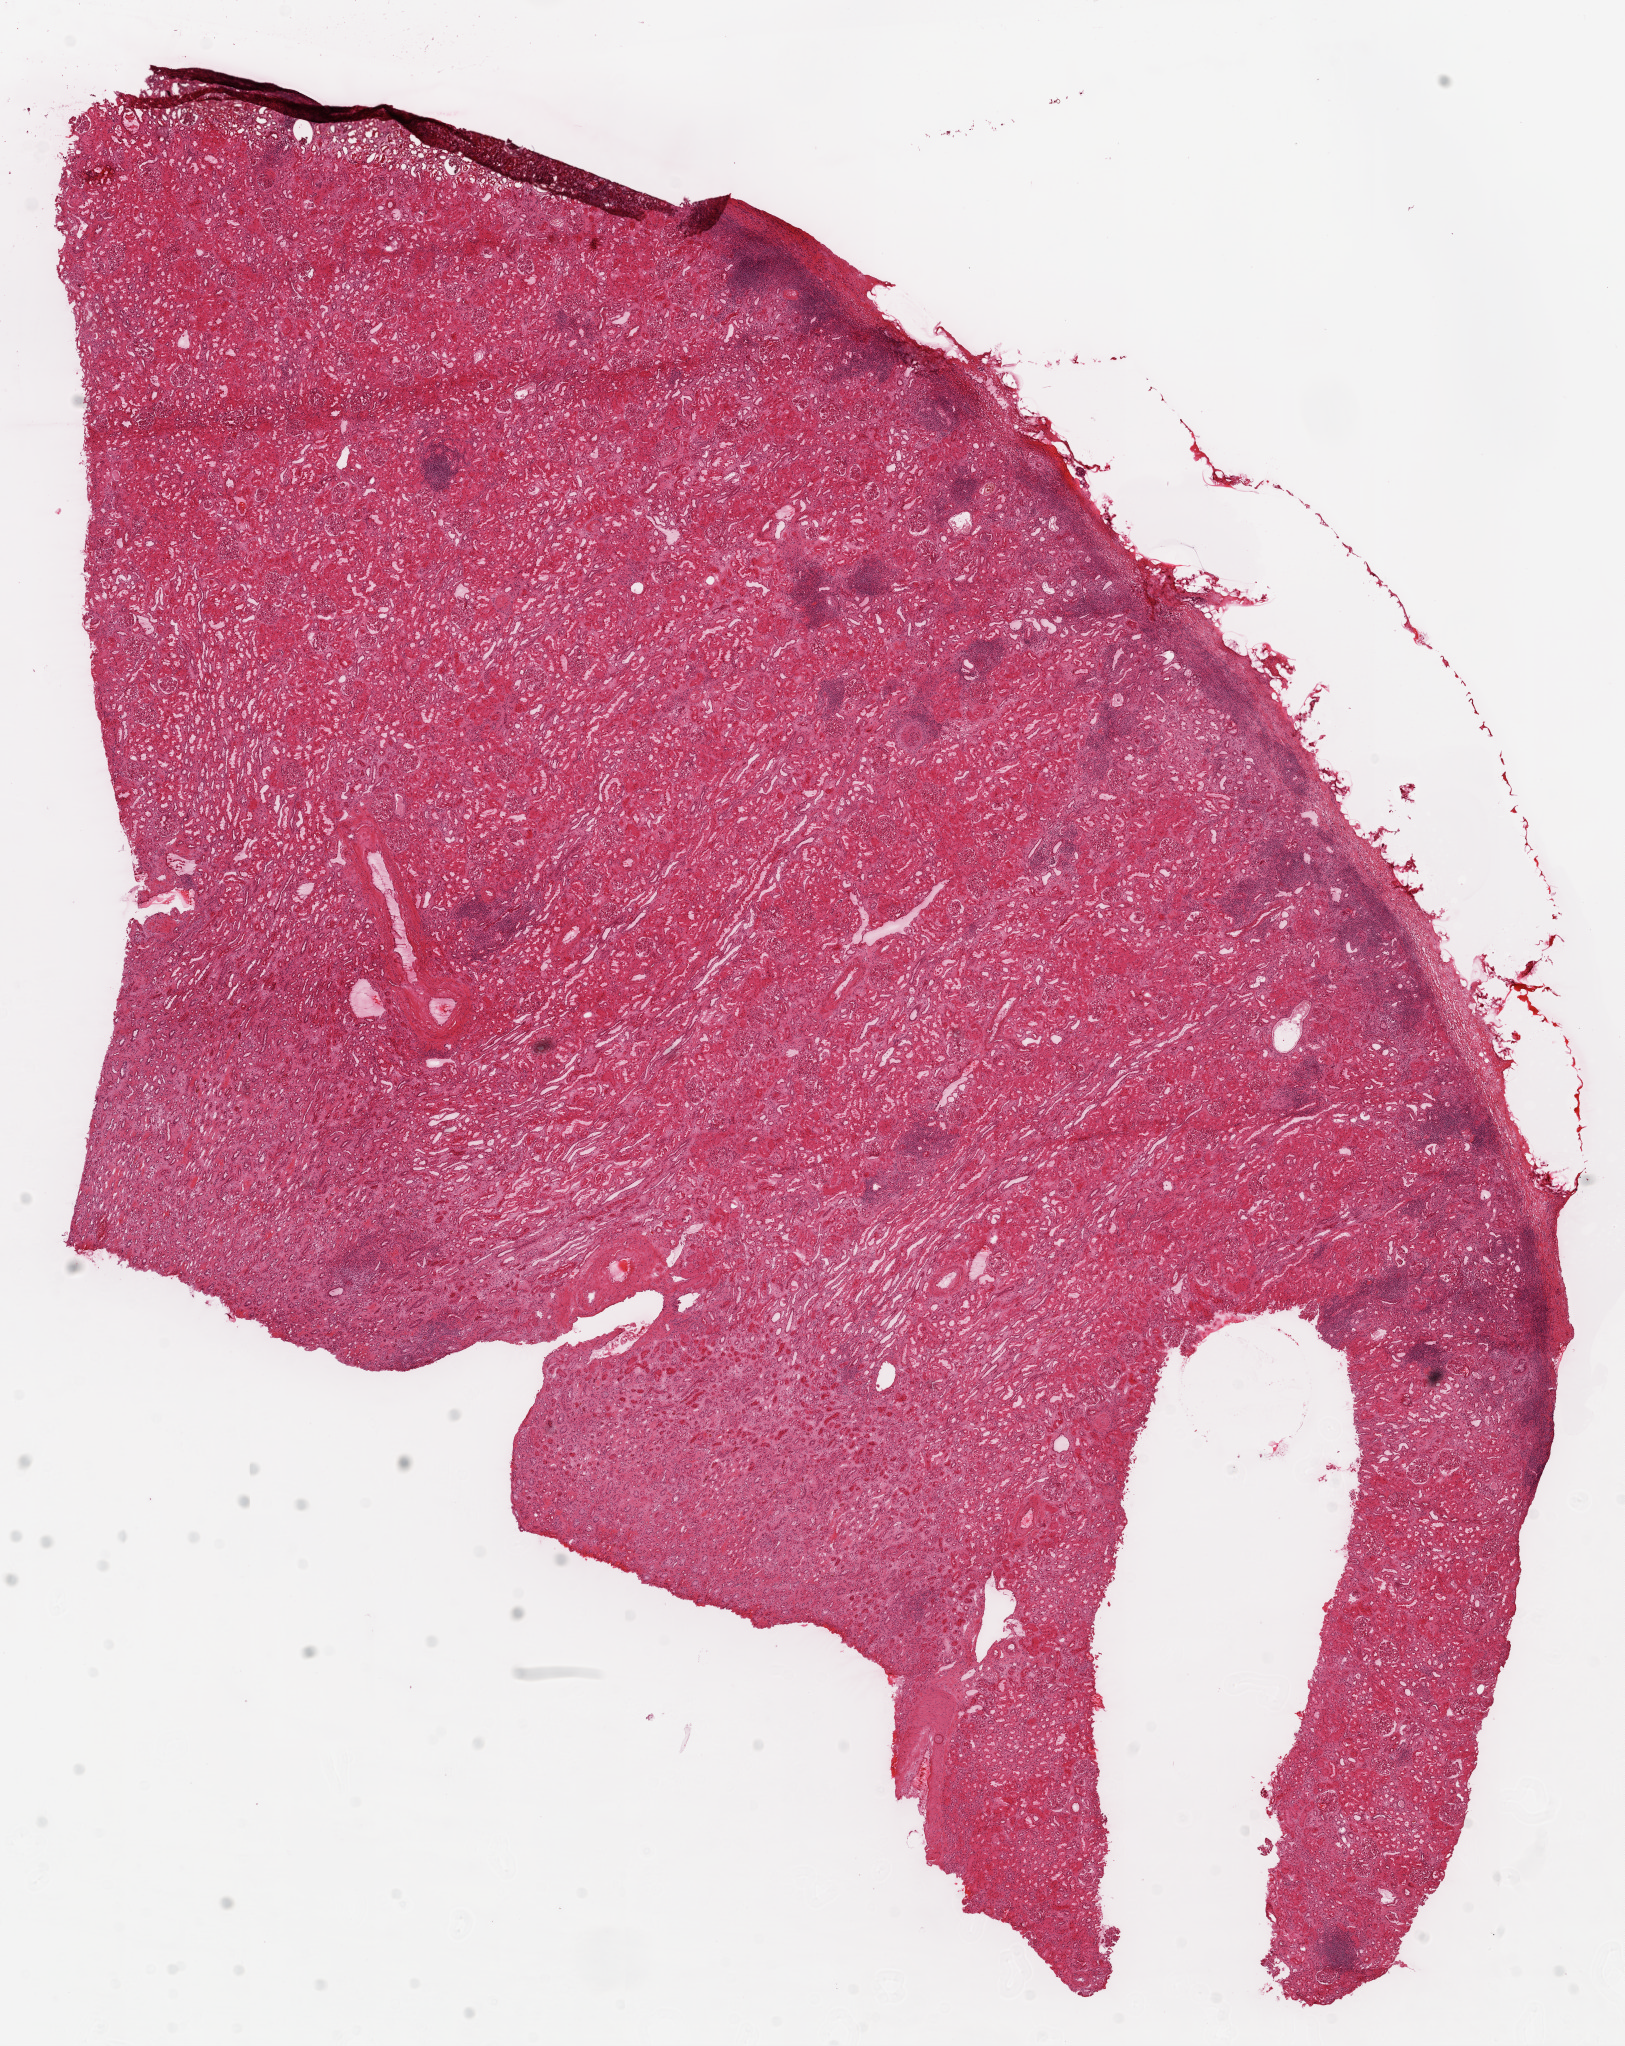
Whole-slide histology image, Hematoxylin and eosin (H&E) stained, whole scanned area (about 13.0 x 16.4 mm, from a 20x scan) shown as a low-resolution overview, frozen section, sample: solid tissue normal (non-tumour tissue), kidney. Male, age 64 years at initial diagnosis.
* this section: solid tissue normal (non-tumour) sample from the same patient
* patient diagnosis: Clear cell adenocarcinoma, NOS